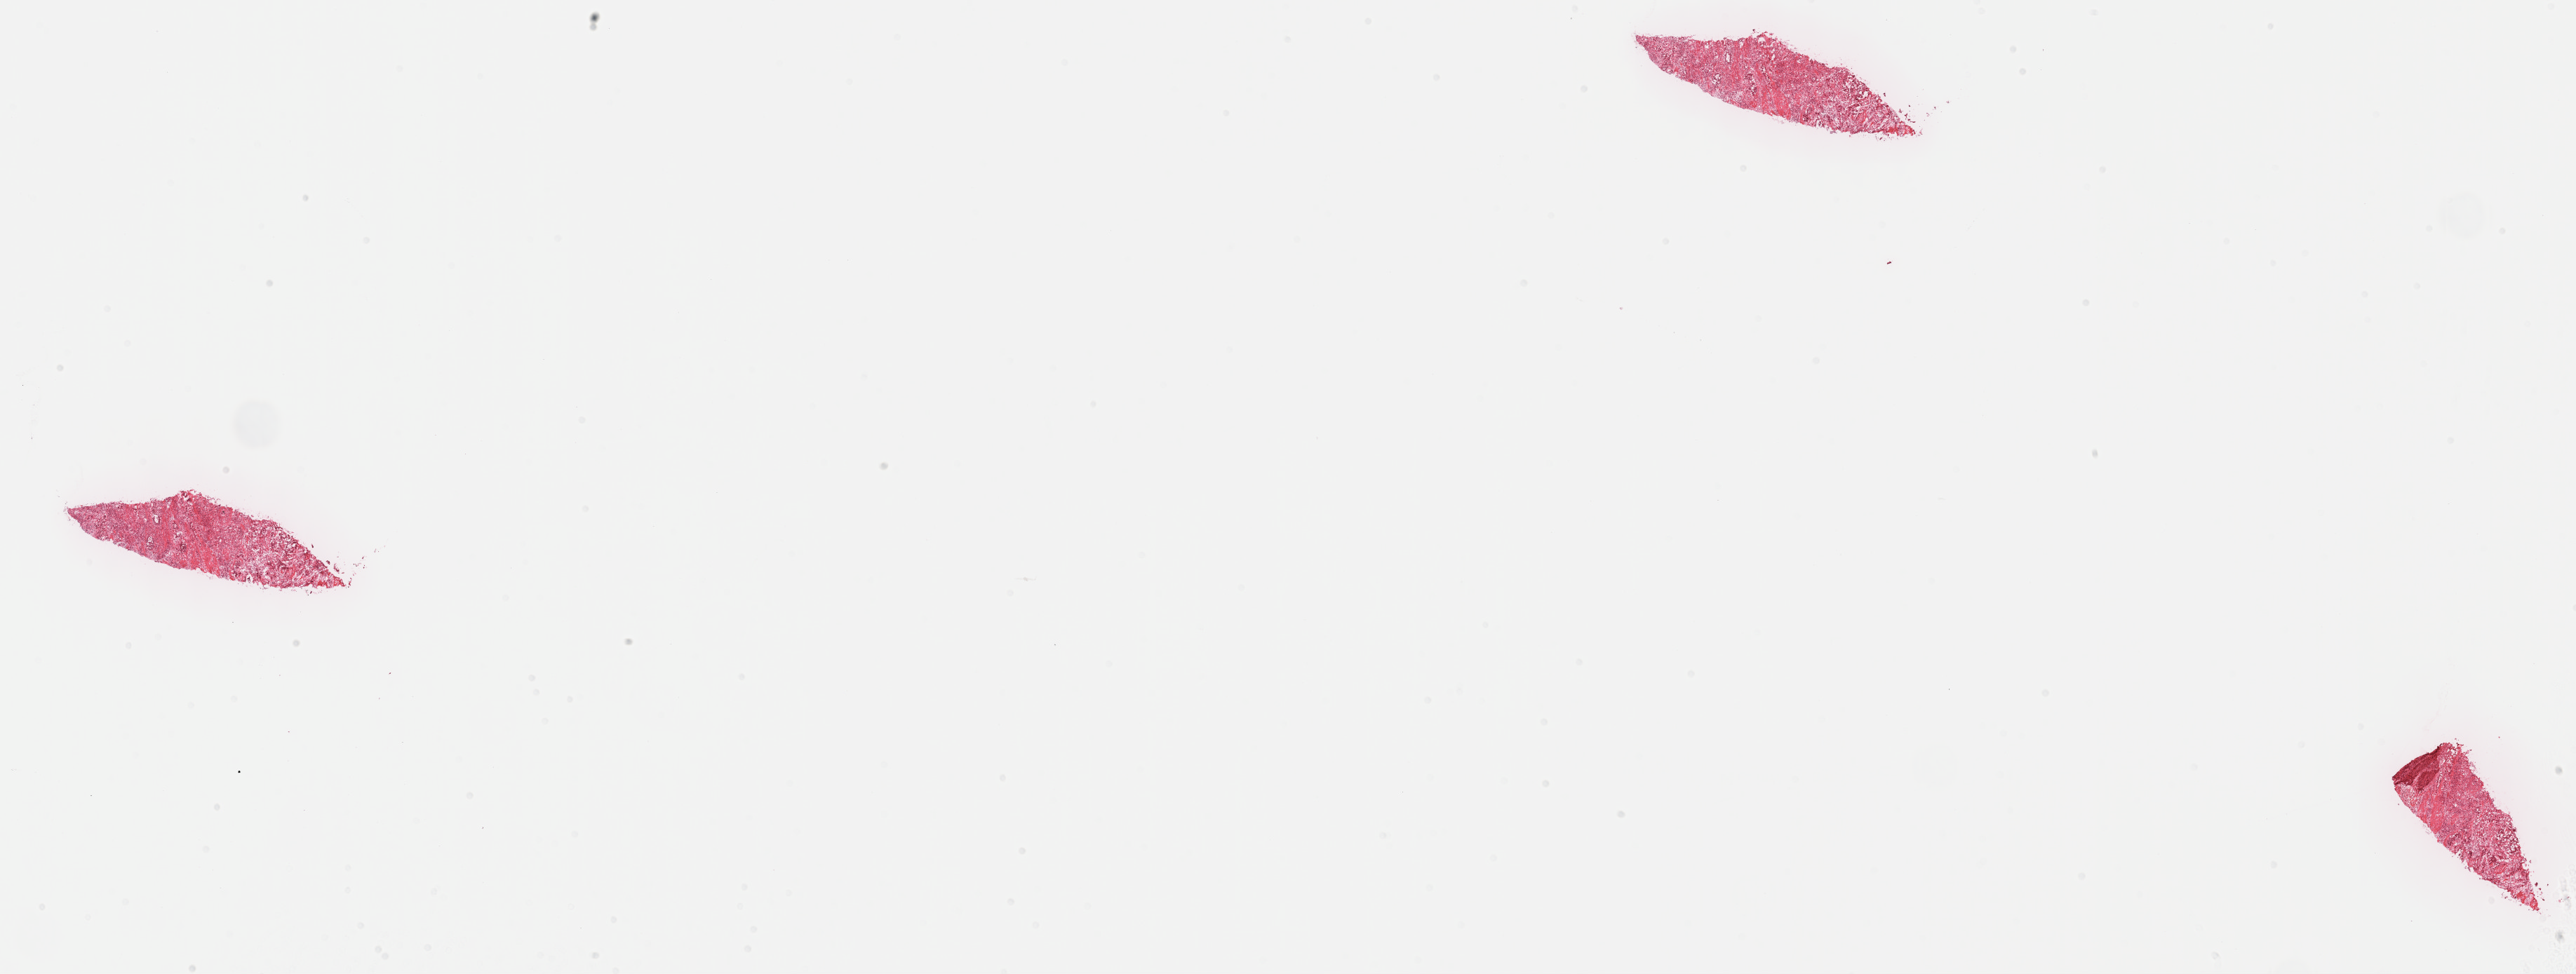
H&E whole-slide image, a low-resolution overview of the entire scanned area, about 29.7 x 11.2 mm. Frozen section. Sample: primary tumour, stomach. Patient: female, age at initial diagnosis 79 years. Slide review estimates, as recorded: tumour cells 70%, tumour nuclei 70%.
Pathologic diagnosis: Tubular adenocarcinoma (gastric antrum).